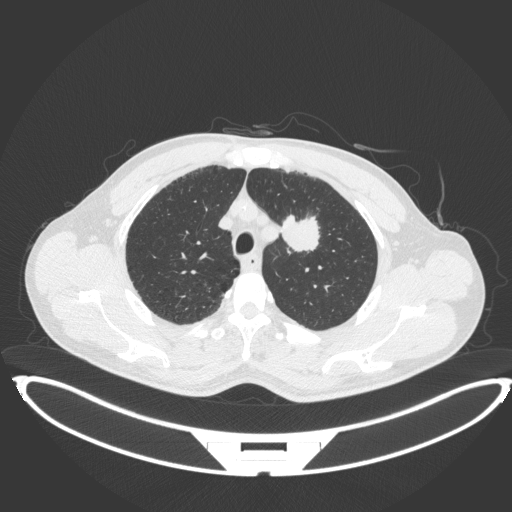
Chest CT, one axial slice; position 346 of 407 along the scan axis; lung window (W 1500 / L -600 HU); 512 × 512 image matrix, field of view 457 × 457 mm. Patient: male, 60 years. From the clinical record (not read from this slice): clinical TNM (as recorded): T2a N0 M0.
Structures marked on this image (bounding box drawn by a radiologist):
- lung tumour (recorded histology: squamous cell carcinoma): bounding box (x1, y1, x2, y2) in pixels: (277, 211, 322, 253)